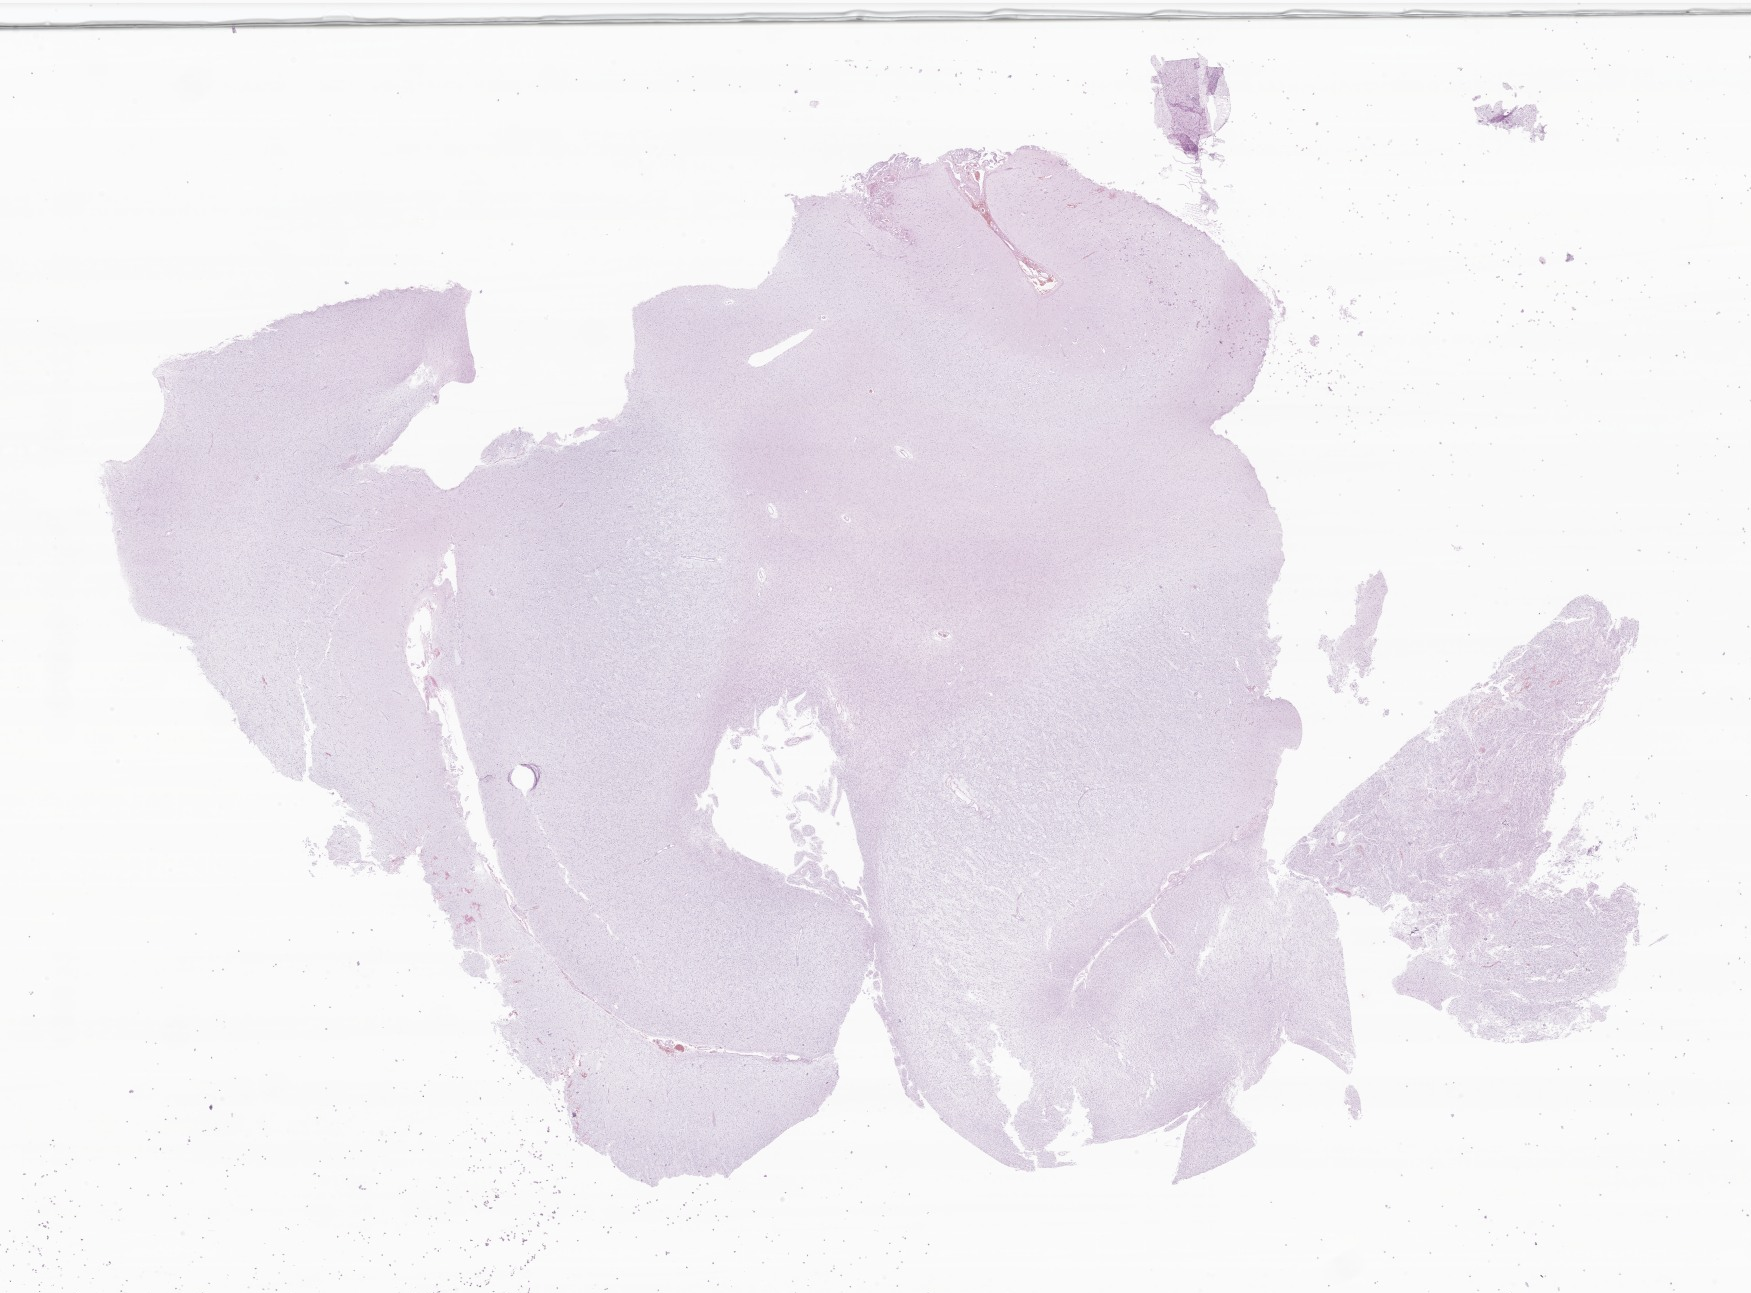
Whole-slide image, H&E stain of tumor tissue from the frontal lobe, a low-resolution overview of the entire scanned area, about 29.5 x 21.8 mm, FFPE section. Female patient, age 64 months (5 years 4 months).
- diagnosis: Dysembryoplastic neuroepithelial tumor